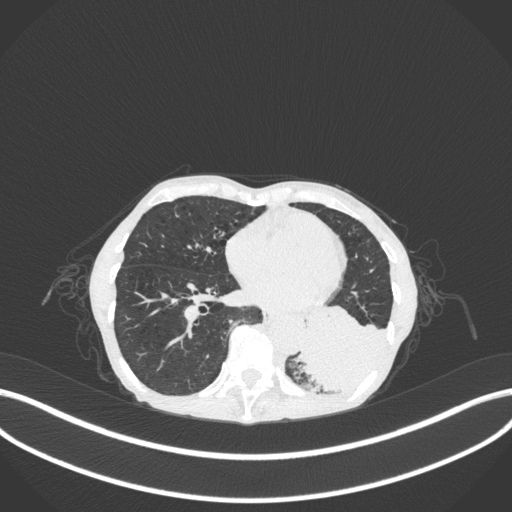
Chest CT, one axial slice; position 95 of 347 along the scan axis; lung window (W 1500 / L -600 HU); 1 mm slice thickness; 512 × 512 image matrix, field of view 400 × 400 mm. Patient: female, 70 years. Case-level facts recorded for this patient, not image findings: clinical TNM (as recorded): T3 N0 M0; histopathological grade: G3.
Structures marked on this image (rectangle marked by the reading radiologist):
- lung tumour (recorded histology: small cell carcinoma): bounding box [x1, y1, x2, y2] px = [292, 301, 391, 395]